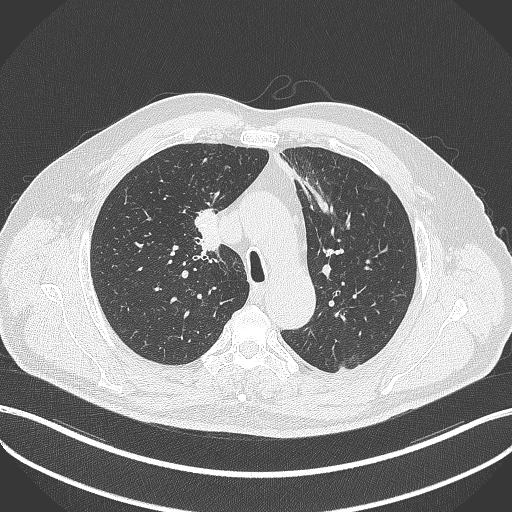
Chest CT, one axial slice. Slice 277 of 411 in the series (ordered by position). Reconstruction kernel B70f. 120 kVp. Lung window (W 1500 / L -600 HU). 1 mm slice thickness. 512 × 512 image matrix, field of view 400 × 400 mm. Male patient, age 60 years. From the clinical record (not read from this slice): clinical TNM (as recorded): T1b N1 M0.
Annotated regions visible in this slice (bounding box drawn by a radiologist):
- lung tumour (recorded histology: squamous cell carcinoma): bounding box (x1, y1, x2, y2) in pixels: (193, 210, 223, 252)